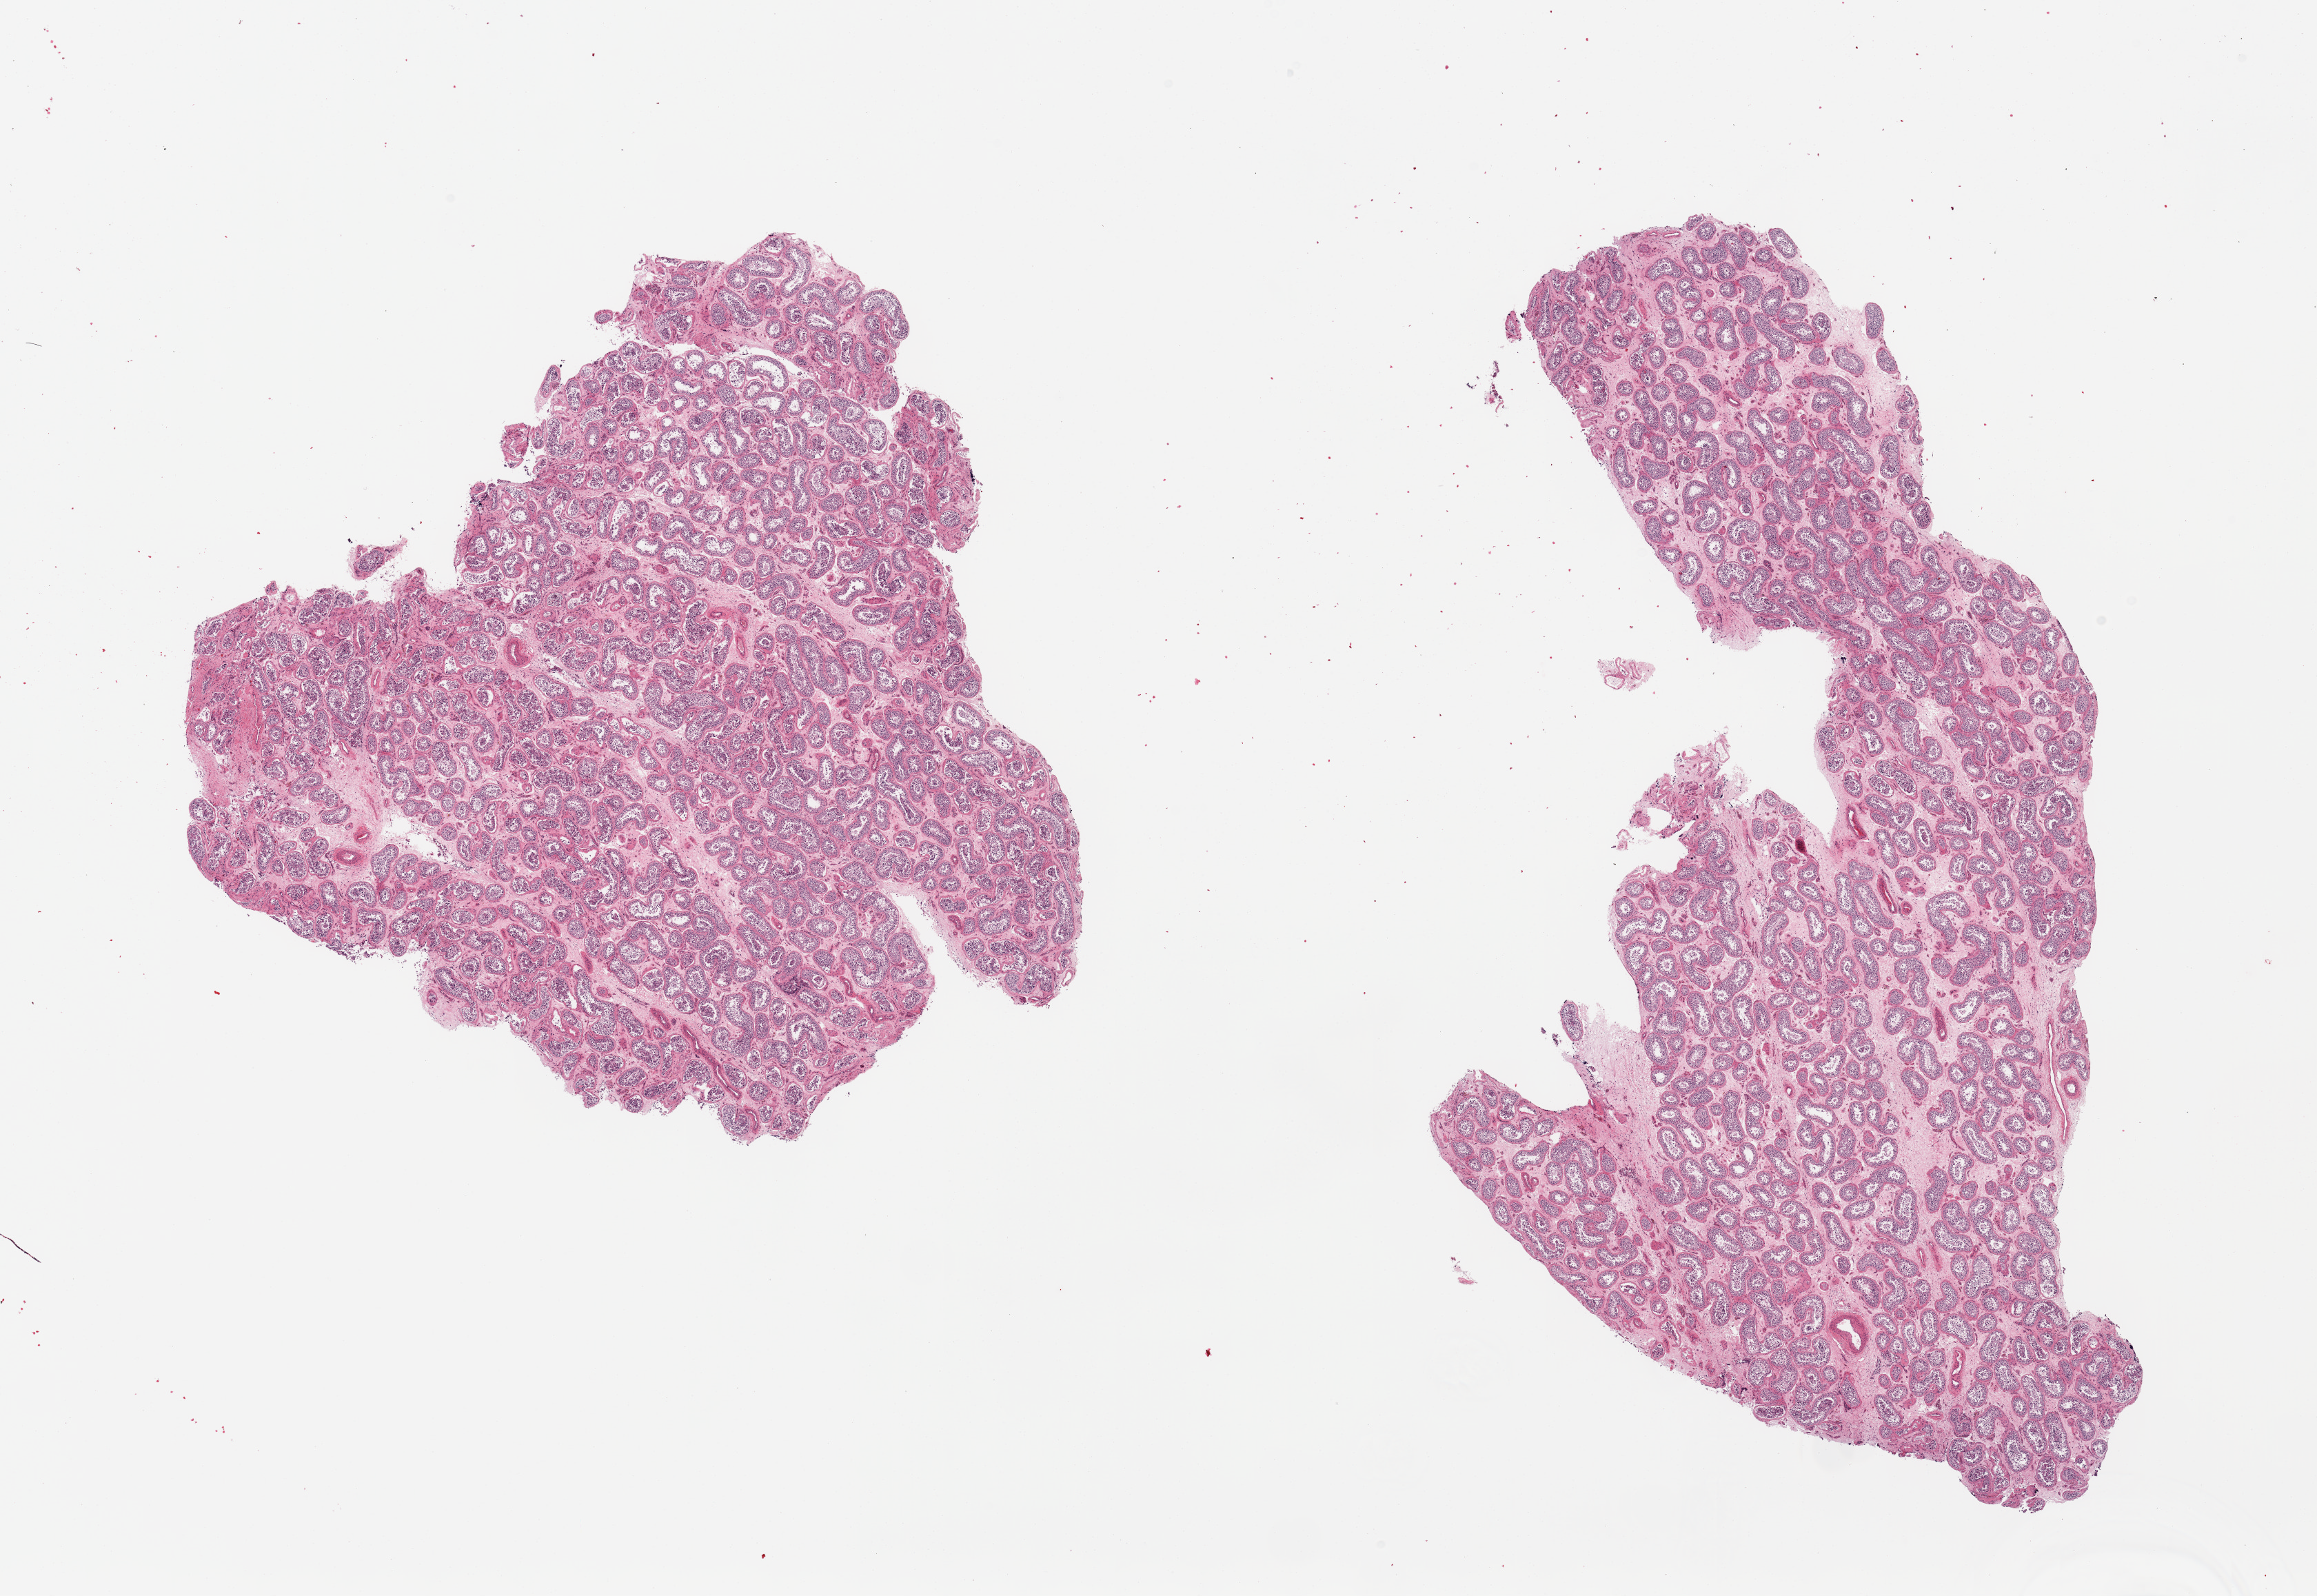
Whole-slide image, haematoxylin and eosin stain, brightfield, a low-resolution overview of the entire scanned area, about 26.6 x 18.3 mm (slide scanned at 20x). PAXgene-fixed, paraffin-embedded tissue. Target tissue: testis. Donor tissue sample. Male donor.
Review note (as recorded): 2 pieces; spermatogenesis.